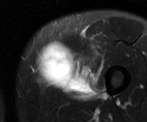
MRI of an extremity soft-tissue mass, one axial slice. Slice 14 of 52 in the series (ordered by position). T2-weighted fat-saturated. MR volume resampled by the dataset authors to the PET/CT grid (not the native acquisition matrix). 3.27 mm slice thickness. 147 × 122 image matrix, field of view 144 × 119 mm. Male patient. Case-level facts recorded for this patient, not image findings: histological type: pleiomorphic liposarcoma; grade: high; site of the primary tumour: left thigh.
Annotated regions visible in this slice (expert contour drawn on MRI and transferred to this co-registered scan by the dataset authors):
- gross tumour volume including surrounding oedema: bounding box (x1, y1, x2, y2) in pixels: (34, 39, 101, 99)
- gross tumour volume (mass): (34, 38, 77, 88)